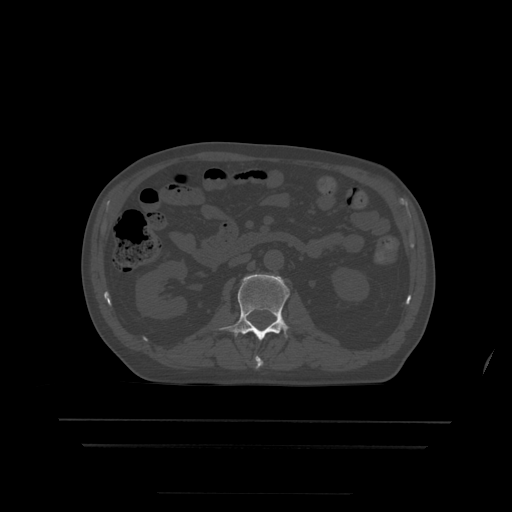
CT including the spine, one axial slice. Position 145 of 522 along the scan axis. Bone window (W 1800 / L 400 HU). 1.25 mm slice thickness. 512 × 512 image matrix, field of view 436 × 436 mm. Patient age 68 years. From the clinical record (not read from this slice): primary cancer: urothelial.
Structures marked on this image (semi-automatic segmentation, software-assisted and operator-edited):
- L1 vertebra: bounding box (x1, y1, x2, y2) in pixels: (255, 356, 263, 369)
- L2 vertebra: (219, 274, 290, 341)